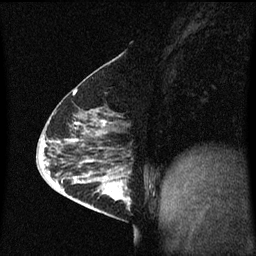
Breast MRI (dynamic contrast-enhanced), one sagittal slice; slice 27 of 60 in the series (ordered by position); dynamic contrast-enhanced series, image 2 of 3 at this slice position (ordered by acquisition); 1.5 T; TE 4.2 ms, TR 8.4 ms; 2 mm slice thickness; 256 × 256 image matrix. Female patient, age 63 years.
Outlined on this slice (semi-automatically segmented with operator editing):
- analysis volume of interest (the breast-tissue region the enhancement analysis was run in; not a lesion): box from (x=98, y=168) to (x=133, y=217) px
- tumour enhancement mask (voxels above the 70 % enhancement threshold inside the analysis volume of interest): (x=98, y=168)–(x=131, y=205)